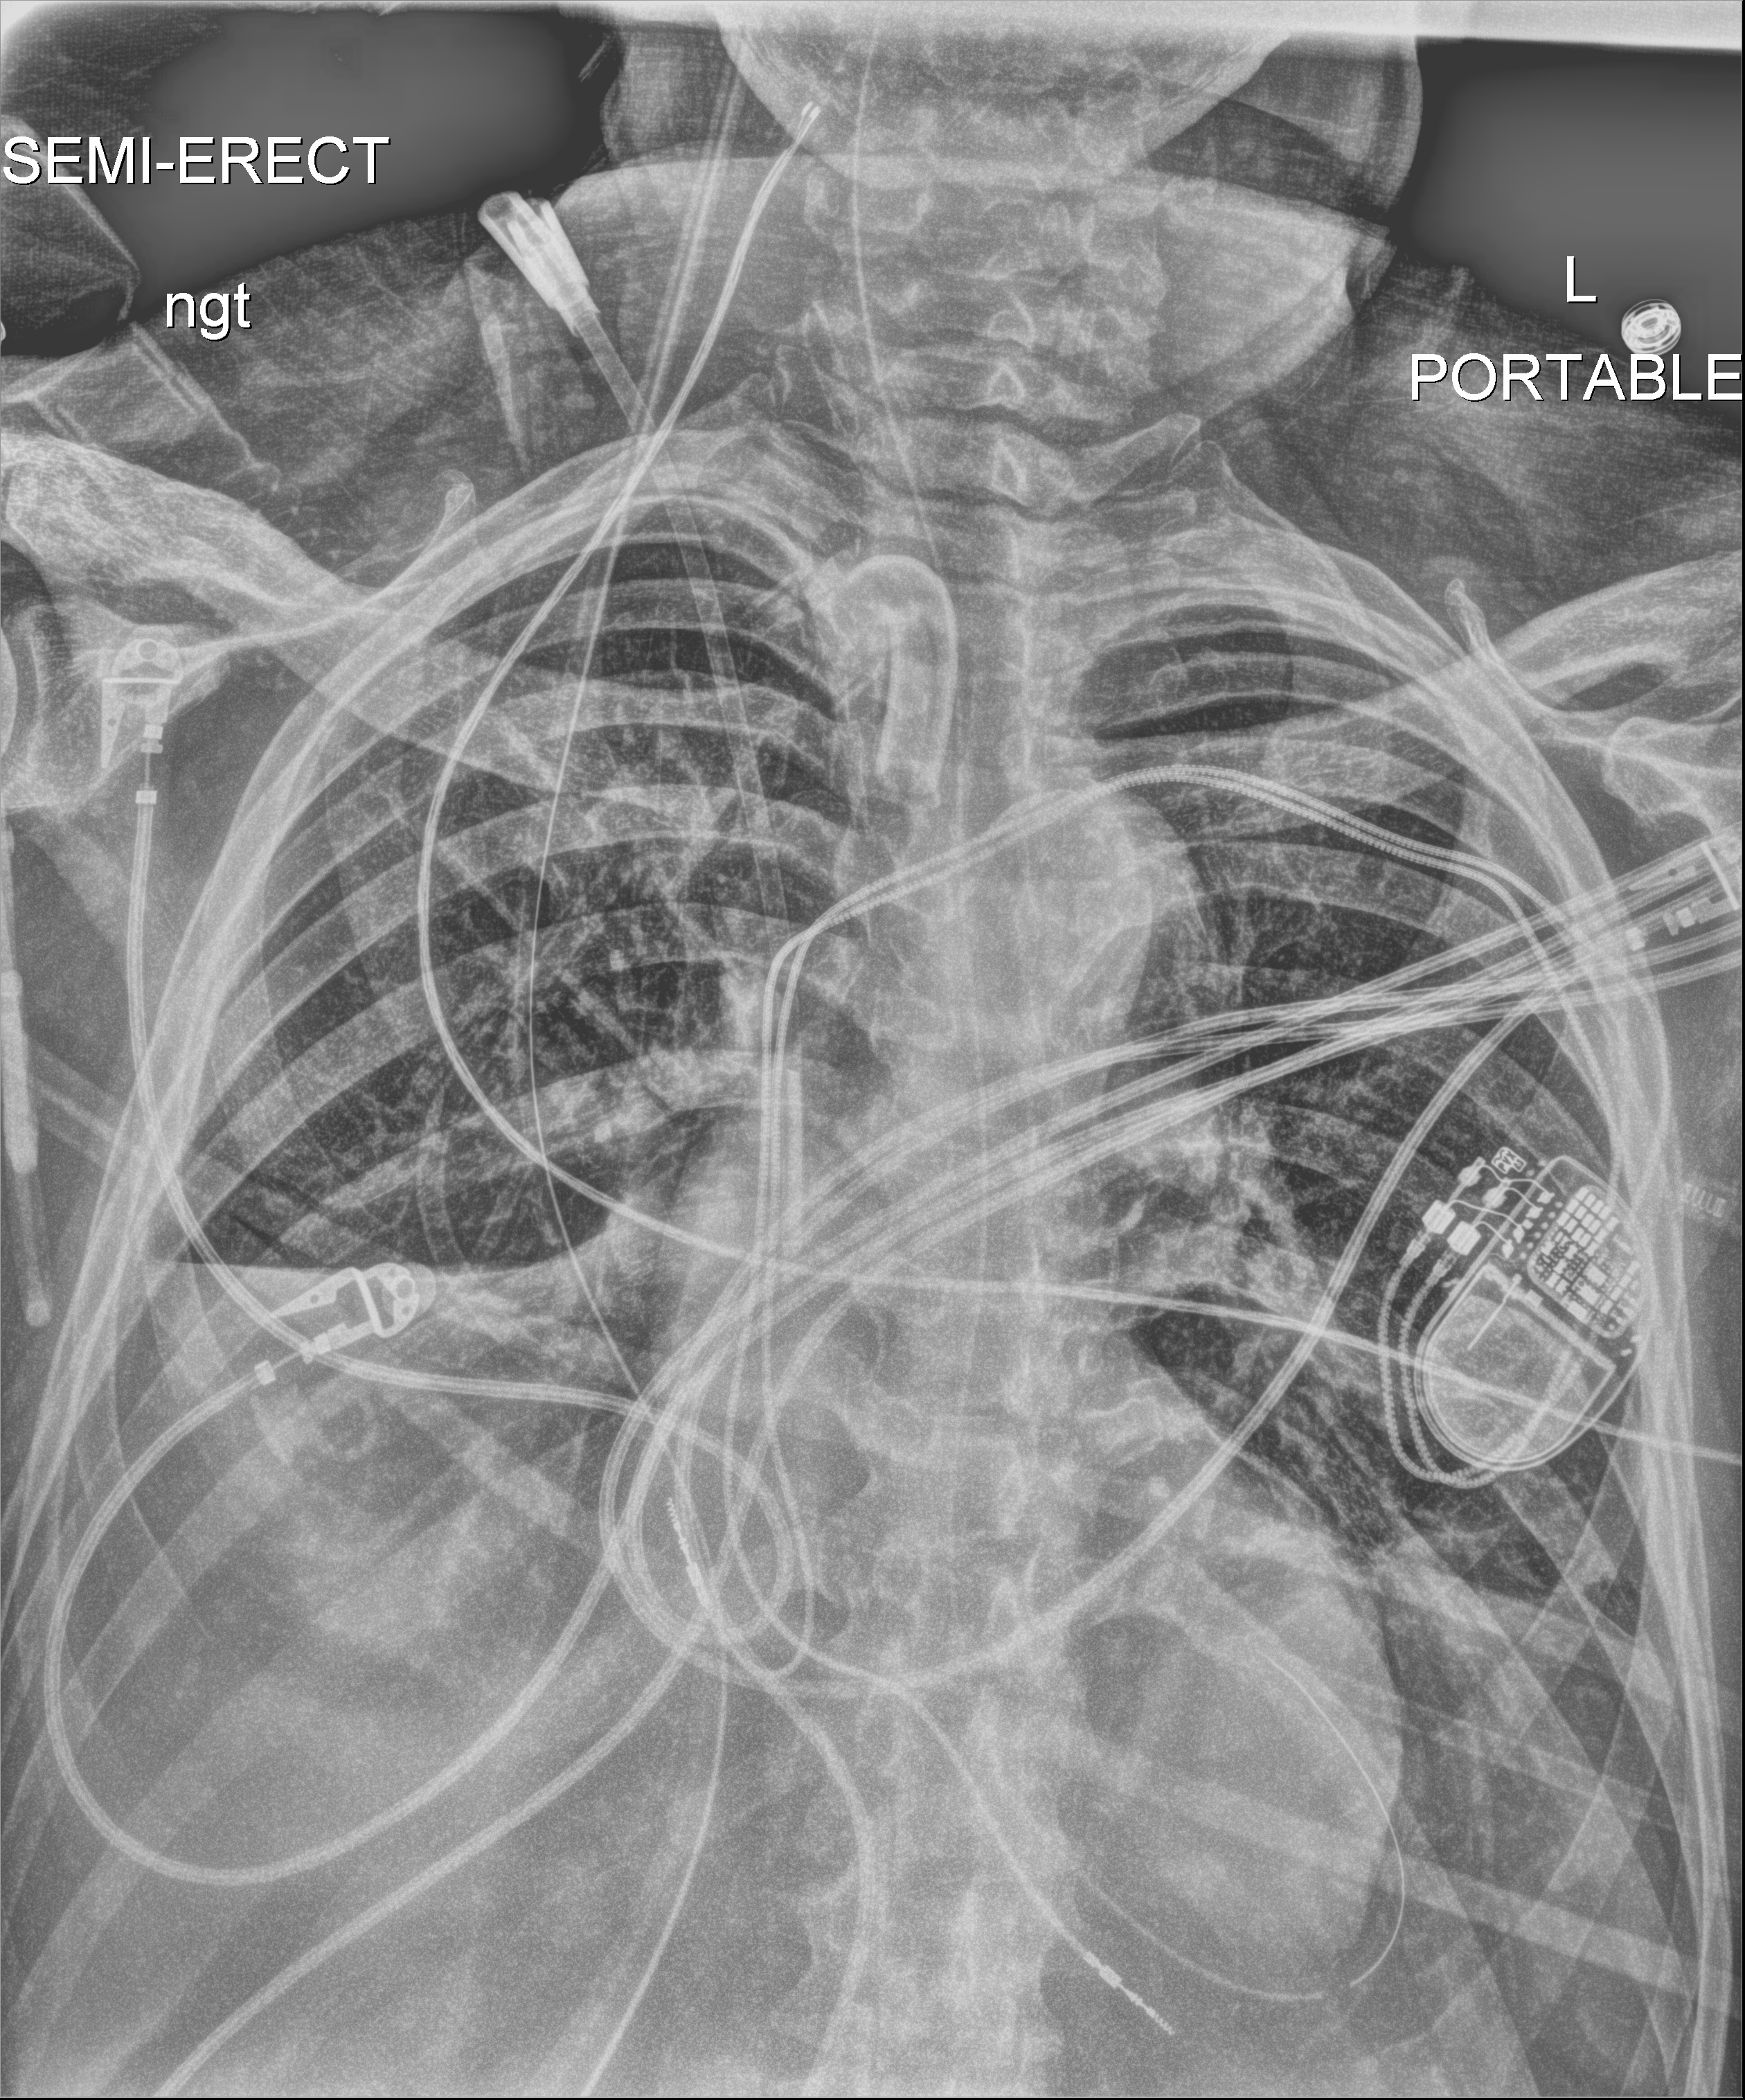
Chest X-ray (portable); anteroposterior (AP) projection. Male patient hospitalised with COVID-19, age 60–74 years.
Admission-level facts for this patient (not findings on this image; timing relative to this image not recorded): length of hospital stay: 41 days; mechanically ventilated during this hospital stay: yes.